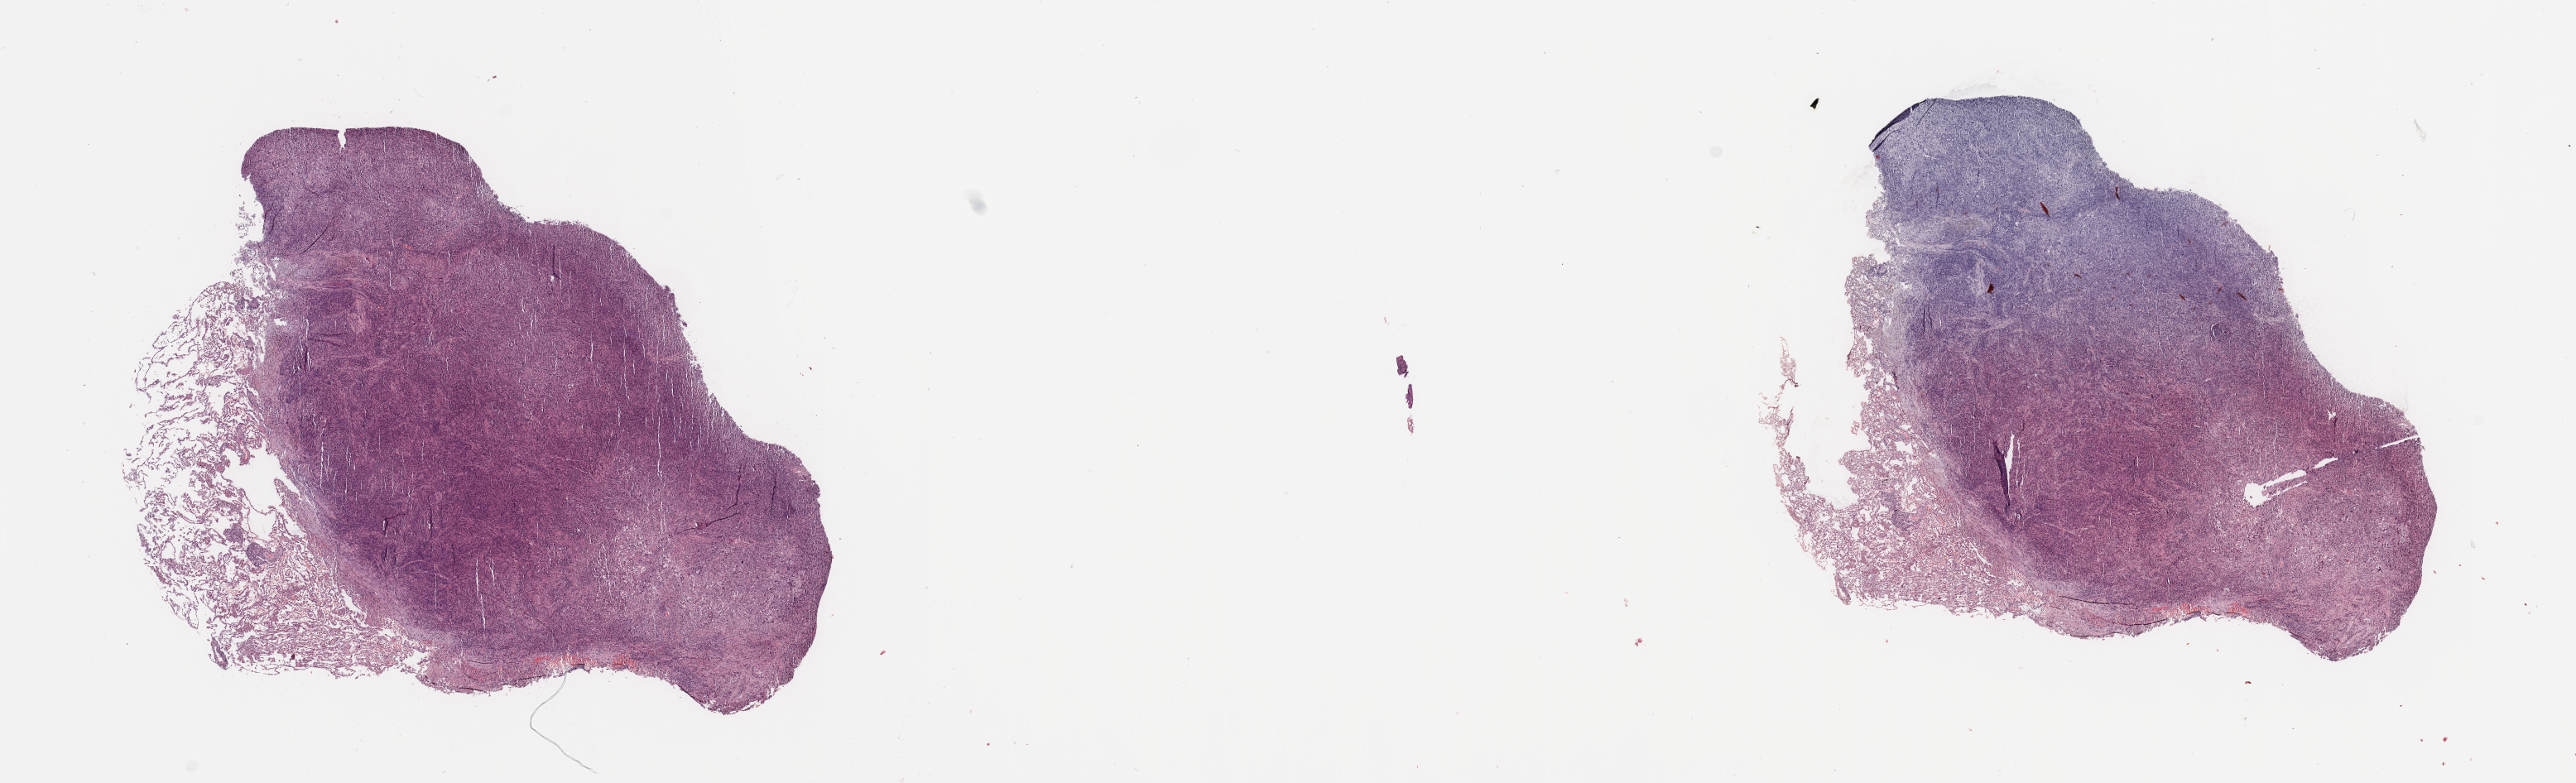
Hematoxylin and eosin (H&E) stained whole-slide image — low-resolution overview of the scanned area, about 24.6 x 7.5 mm; tumour tissue sample, lung. 64-year-old male patient. Histologic grade: G3 (poorly differentiated).
AJCC pathologic stage: IA1. Histologic diagnosis: Adenocarcinoma, NOS.